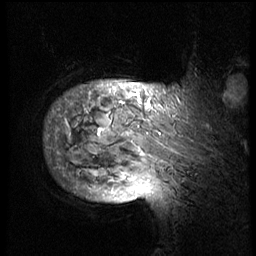
Breast MRI (dynamic contrast-enhanced), one sagittal slice. Position 64 of 74 along the scan axis. 3 images stored at this slice position (order not interpretable as contrast timing). 1.5 T. TE 4.2 ms, TR 8.9 ms. 256 × 256 image matrix. Patient: female, 57 years. Case-level facts recorded for this patient, not image findings: setting: breast cancer imaged before/during neoadjuvant chemotherapy; receptor status: HER2-positive.
Structures marked on this image (semi-automatically segmented with operator editing):
- analysis volume of interest (the breast-tissue region the enhancement analysis was run in; not a lesion): box from (x=44, y=62) to (x=235, y=175) px
- tumour enhancement mask (voxels above the 140 % enhancement threshold inside the analysis volume of interest): (x=64, y=86)–(x=179, y=157)